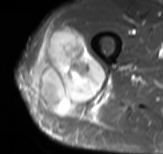
MRI of an extremity soft-tissue mass, one axial slice; position 40 of 61 along the scan axis; STIR; MR volume resampled by the dataset authors to the PET/CT grid (not the native acquisition matrix); 3.27 mm slice thickness; 163 × 154 image matrix, field of view 159 × 150 mm. Male patient. Case-level facts recorded for this patient, not image findings: histological type: poorly differentiated synovial sarcoma; grade: high; site of the primary tumour: right buttock.
Structures marked on this image (expert contour drawn on MRI and transferred to this co-registered scan by the dataset authors):
- gross tumour volume including surrounding oedema: bounding box [x1, y1, x2, y2] px = [34, 25, 108, 118]
- gross tumour volume (mass): [37, 25, 106, 115]